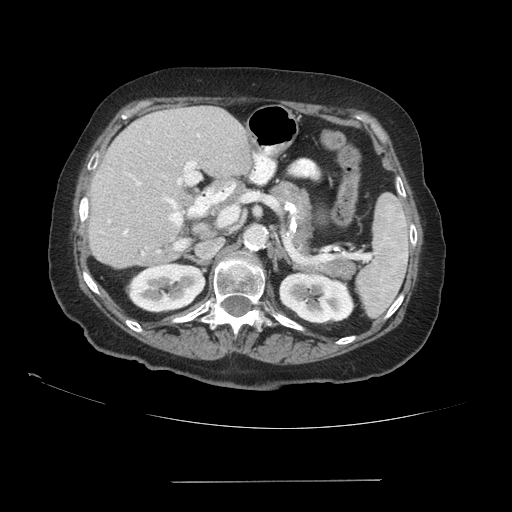
Contrast-enhanced abdominal CT (liver protocol), one axial slice; position 53 of 89 along the scan axis; soft-tissue window (W 400 / L 40 HU); 2.5 mm slice thickness; 512 × 512 image matrix, field of view 400 × 400 mm. Case-level facts recorded for this patient, not image findings: diagnosis: hepatocellular carcinoma (patient treated with transarterial chemoembolisation; whether this scan precedes or follows treatment is not stated here); TNM stage (as recorded): Stage-IVA; Child-Pugh class: A; tumour differentiation: poorly differentiated.
Outlined on this slice (semi-automatically segmented with operator editing):
- liver parenchyma outside the tumour (the mass and vessels are separate outlines, so this box may not span the whole liver): bounding box [x1, y1, x2, y2] px = [88, 106, 252, 268]
- liver vessels: [108, 134, 200, 255]